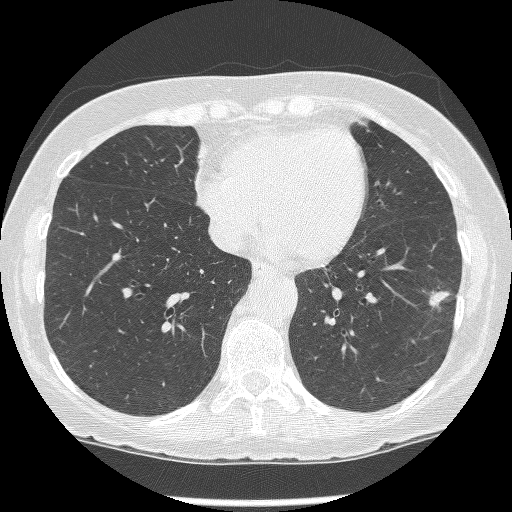
Chest CT (low-dose screening protocol), one axial image. First (baseline) screen. Lung window (W 1500 / L -600 HU). 1.25 mm slice thickness. Slice 85 of 247 in the series. 512 × 512 image matrix. Female, age 62 years at enrolment. Former smoker at enrolment.
- Expert reader's lesion annotation, bounding box <421,281,463,325> (left, top, right, bottom; pixels).
- The screening reader recorded 2 non-calcified nodules or masses ≥4 mm on this exam; which of them this box marks is not recorded.
- Lung cancer was diagnosed 15 days after this screen: non-small cell carcinoma, left lower lobe, stage IIIB (AJCC 6th edition), 23 mm at pathology.